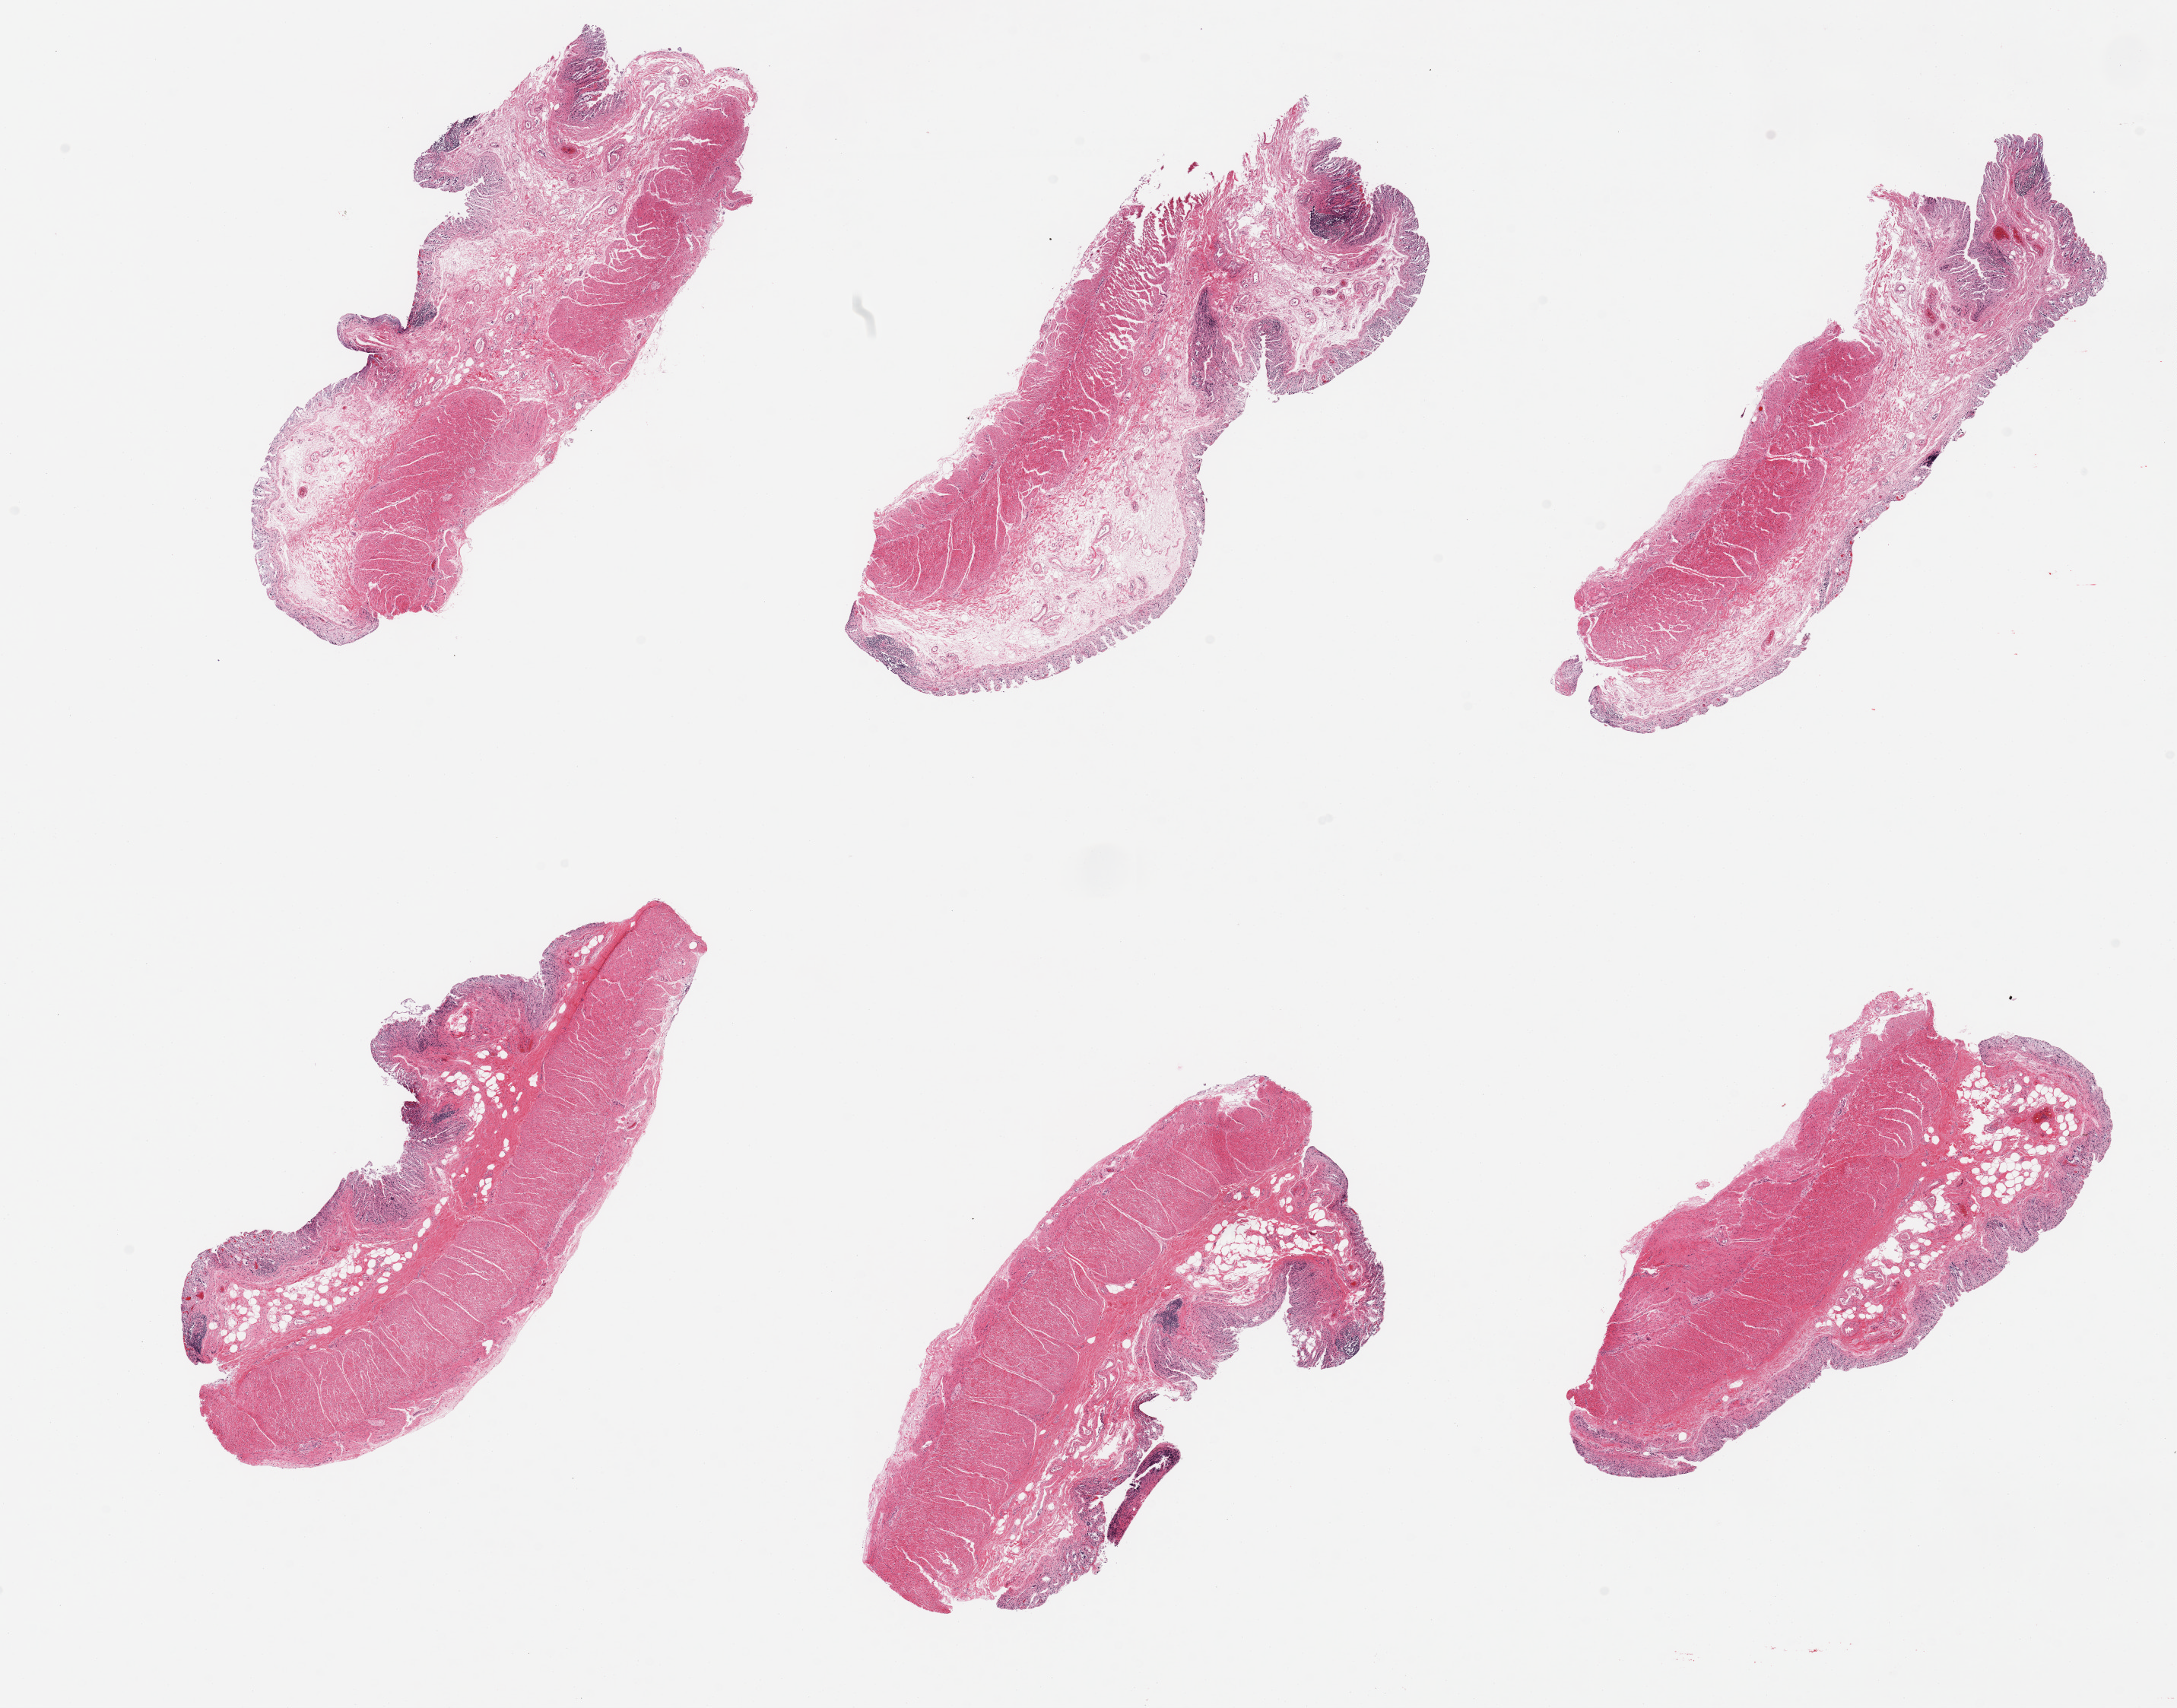
Digitized haematoxylin and eosin-stained section, brightfield, shown as a low-resolution overview of the whole scanned area (about 22.6 x 17.8 mm, acquisition: 20x scan). PAXgene-fixed, paraffin-embedded tissue. Target tissue: transverse colon. Donor tissue sample. Donor: male.
• review note (as recorded): 6 pieces, mcuosa up to ~0.2mm, sloughing; glandular elements of mucosa totally autolyzed